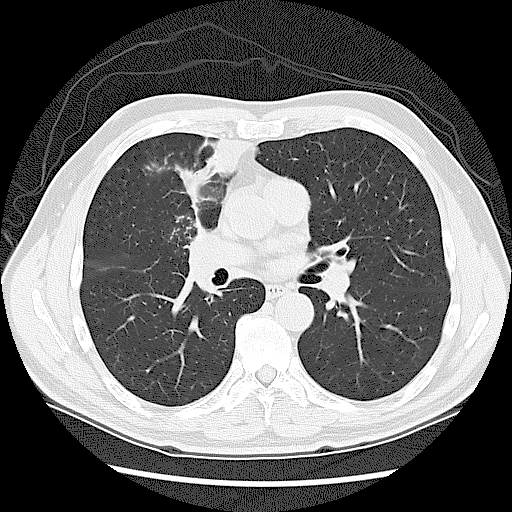
Low-dose screening chest CT, axial slice, baseline annual screen, lung window (W 1500 / L -600 HU), lung (sharp) reconstruction kernel (LUNG), slice 63 of 131 in the series. Male, age 60 years at enrolment. Current smoker at enrolment.
• Expert-annotated lung lesion, bounding box (x1, y1, x2, y2) in pixels: (158, 214, 240, 303).
• Screening reader's record for this exam: no non-calcified nodule ≥4 mm recorded.
• Participant outcome: lung cancer diagnosed 41 days after this screen — small cell carcinoma, NOS, right upper lobe, stage IIIA (AJCC 6th edition).